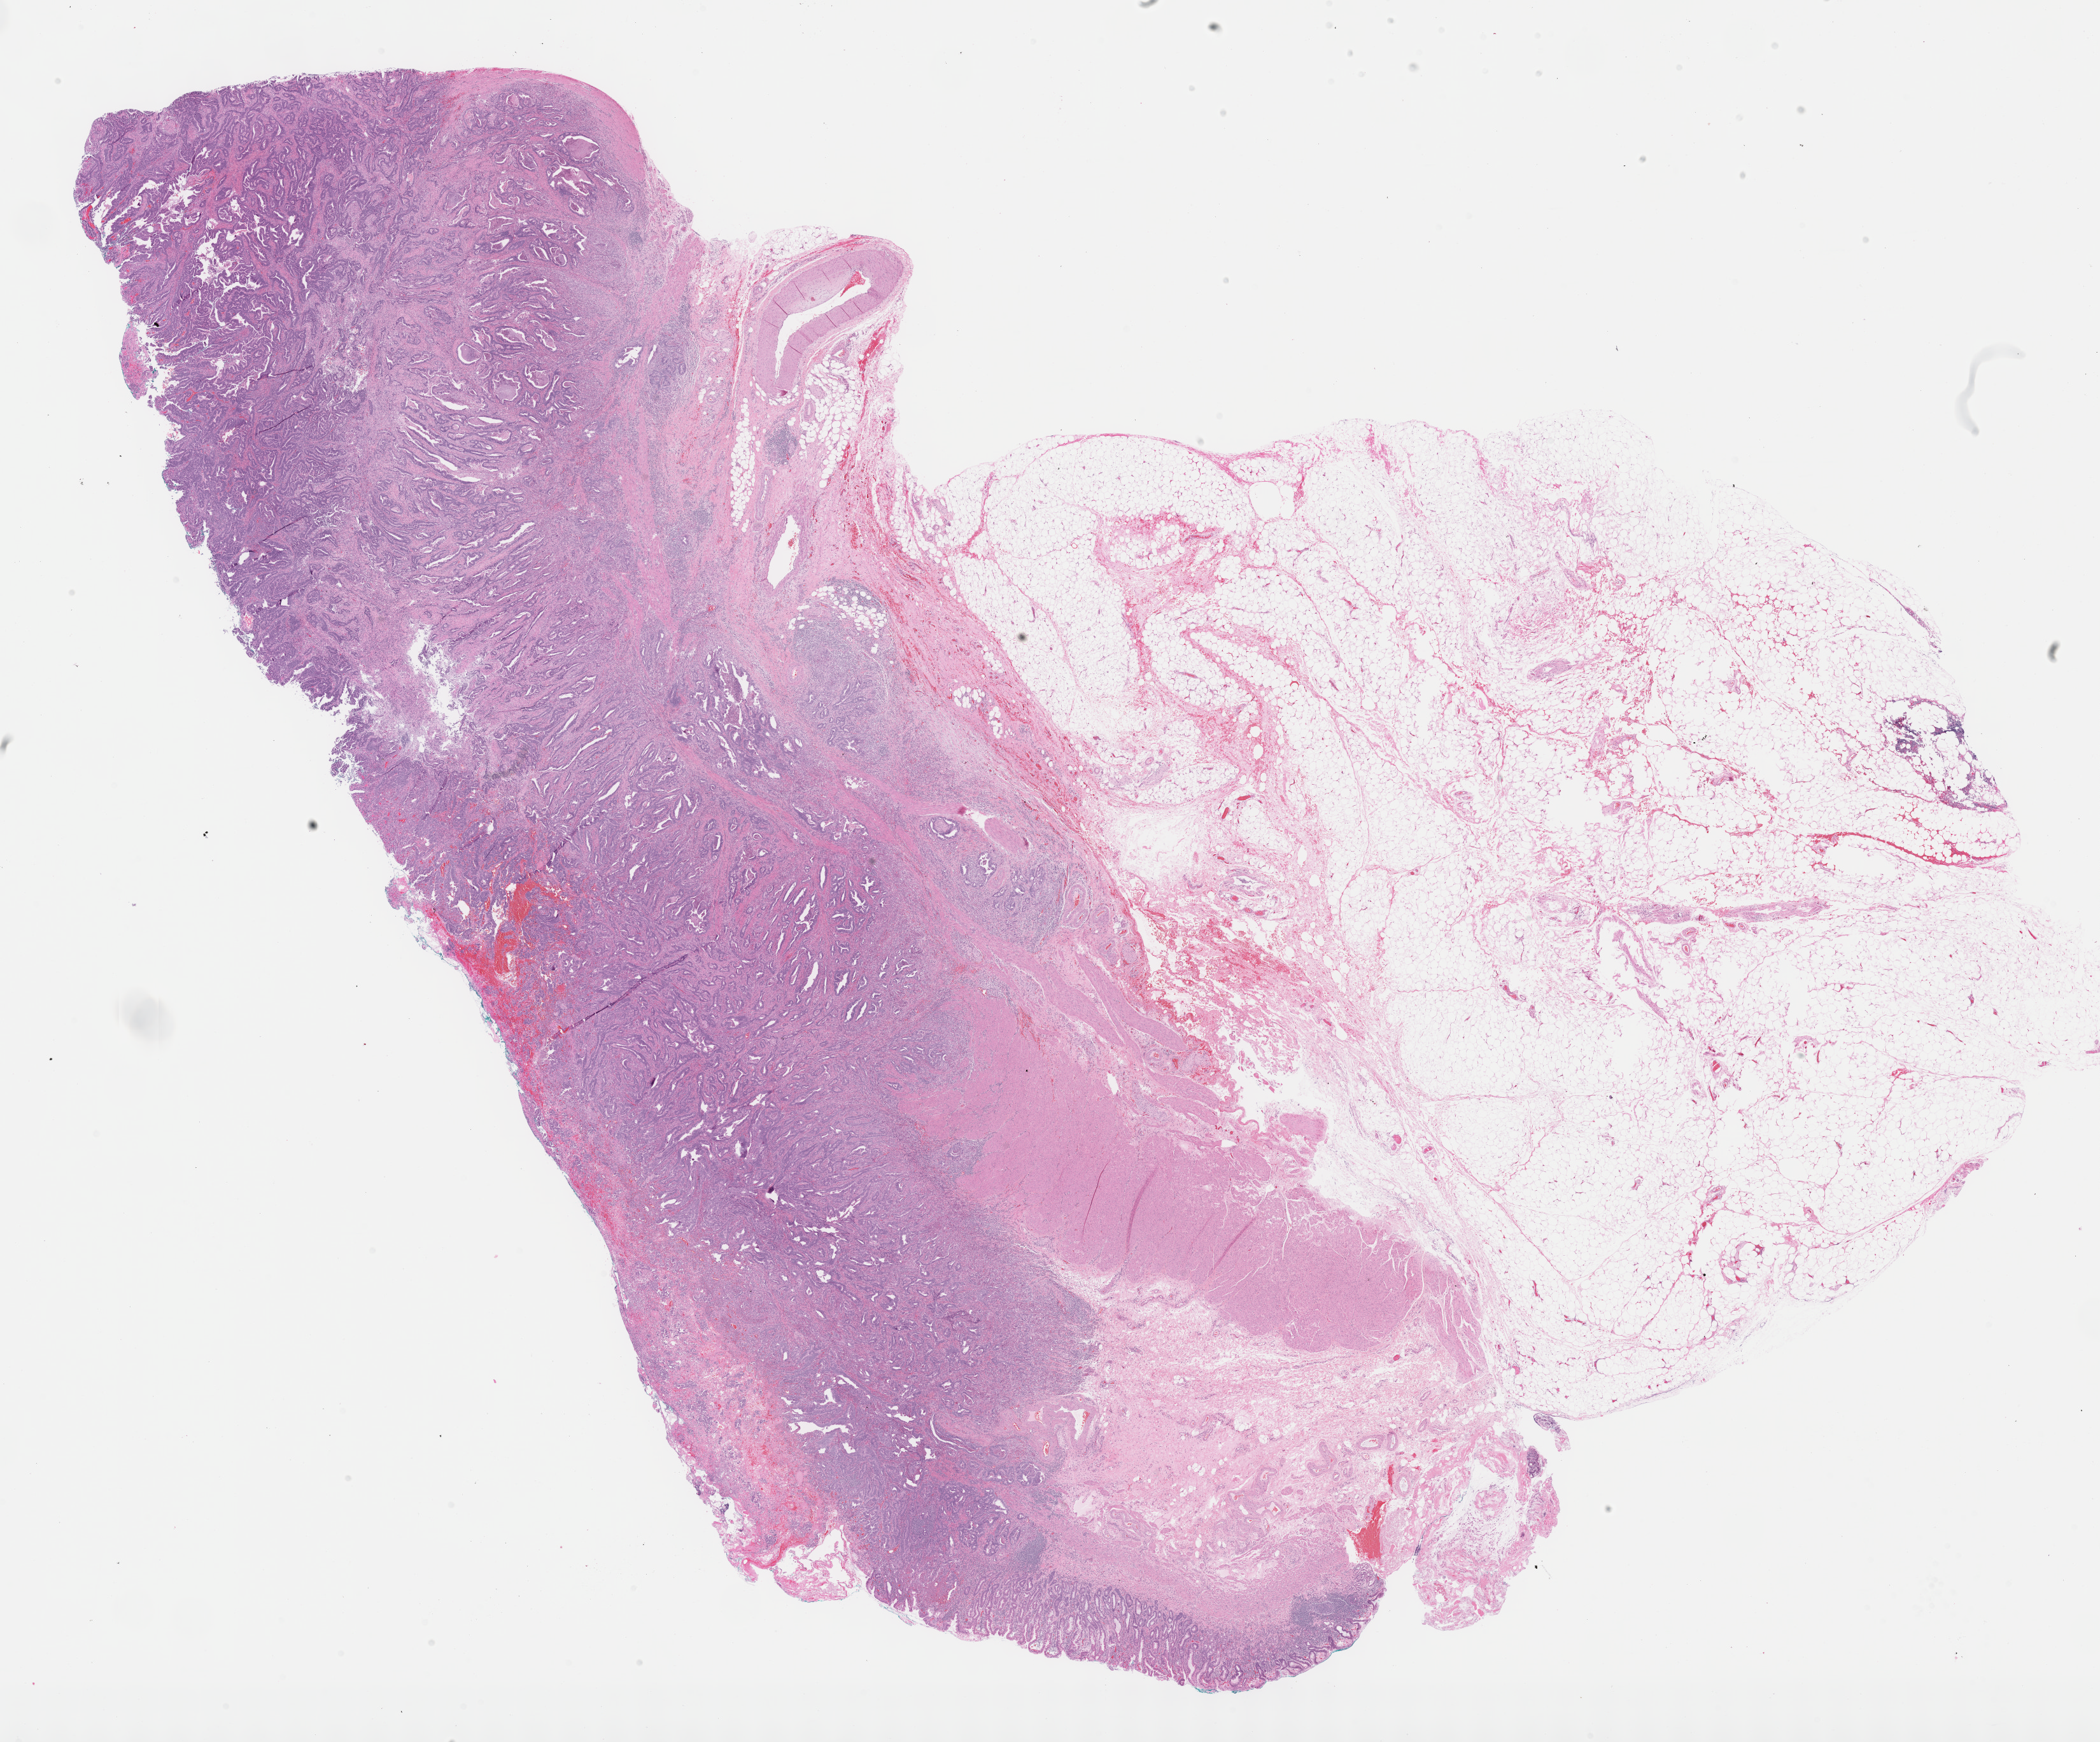
Digitized H&E-stained tissue section (whole slide), shown as a low-resolution overview of the whole scanned area (about 26.7 x 22.1 mm, acquisition: 40x scan). FFPE section. Sample: primary tumour, stomach. Male patient; age at initial diagnosis 70 years. Histologic grade: G2 (moderately differentiated).
- AJCC pathologic stage: IB (6th edition)
- lymph nodes positive (case pathology): 0 of 15 examined
- diagnosis: Adenocarcinoma, NOS (lesser curvature of stomach, NOS)